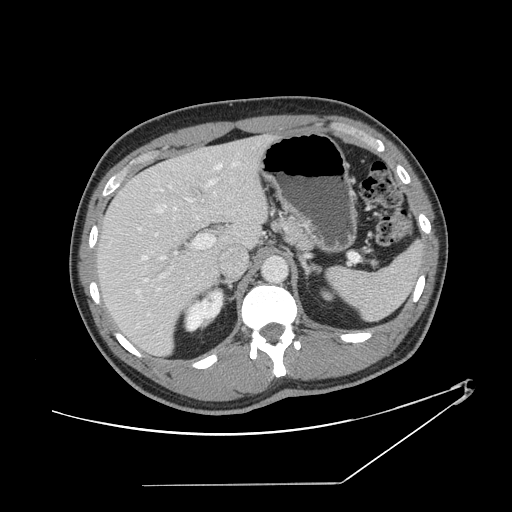
Contrast-enhanced abdominal CT, one axial slice. Slice 90 of 152 in the series (ordered by position). Reconstruction kernel STANDARD. 120 kVp. Intravenous contrast given. Soft-tissue window (W 400 / L 40 HU). 2.5 mm slice thickness. 512 × 512 image matrix, field of view 432 × 432 mm. Male patient, age 45 years. From the clinical record (not read from this slice): diagnosis: colorectal cancer liver metastases, imaged before liver resection; multiple liver metastases: no; largest metastasis: 1 cm; disease in both lobes: no.
Annotated regions visible in this slice (expert manual segmentation):
- hepatic veins: bounding box (x1, y1, x2, y2) in pixels: (111, 162, 223, 294)
- liver: (98, 137, 267, 355)
- planned liver remnant (the part of the liver to remain after resection): (98, 155, 226, 355)
- portal vein (with intrahepatic branches): (138, 163, 235, 316)